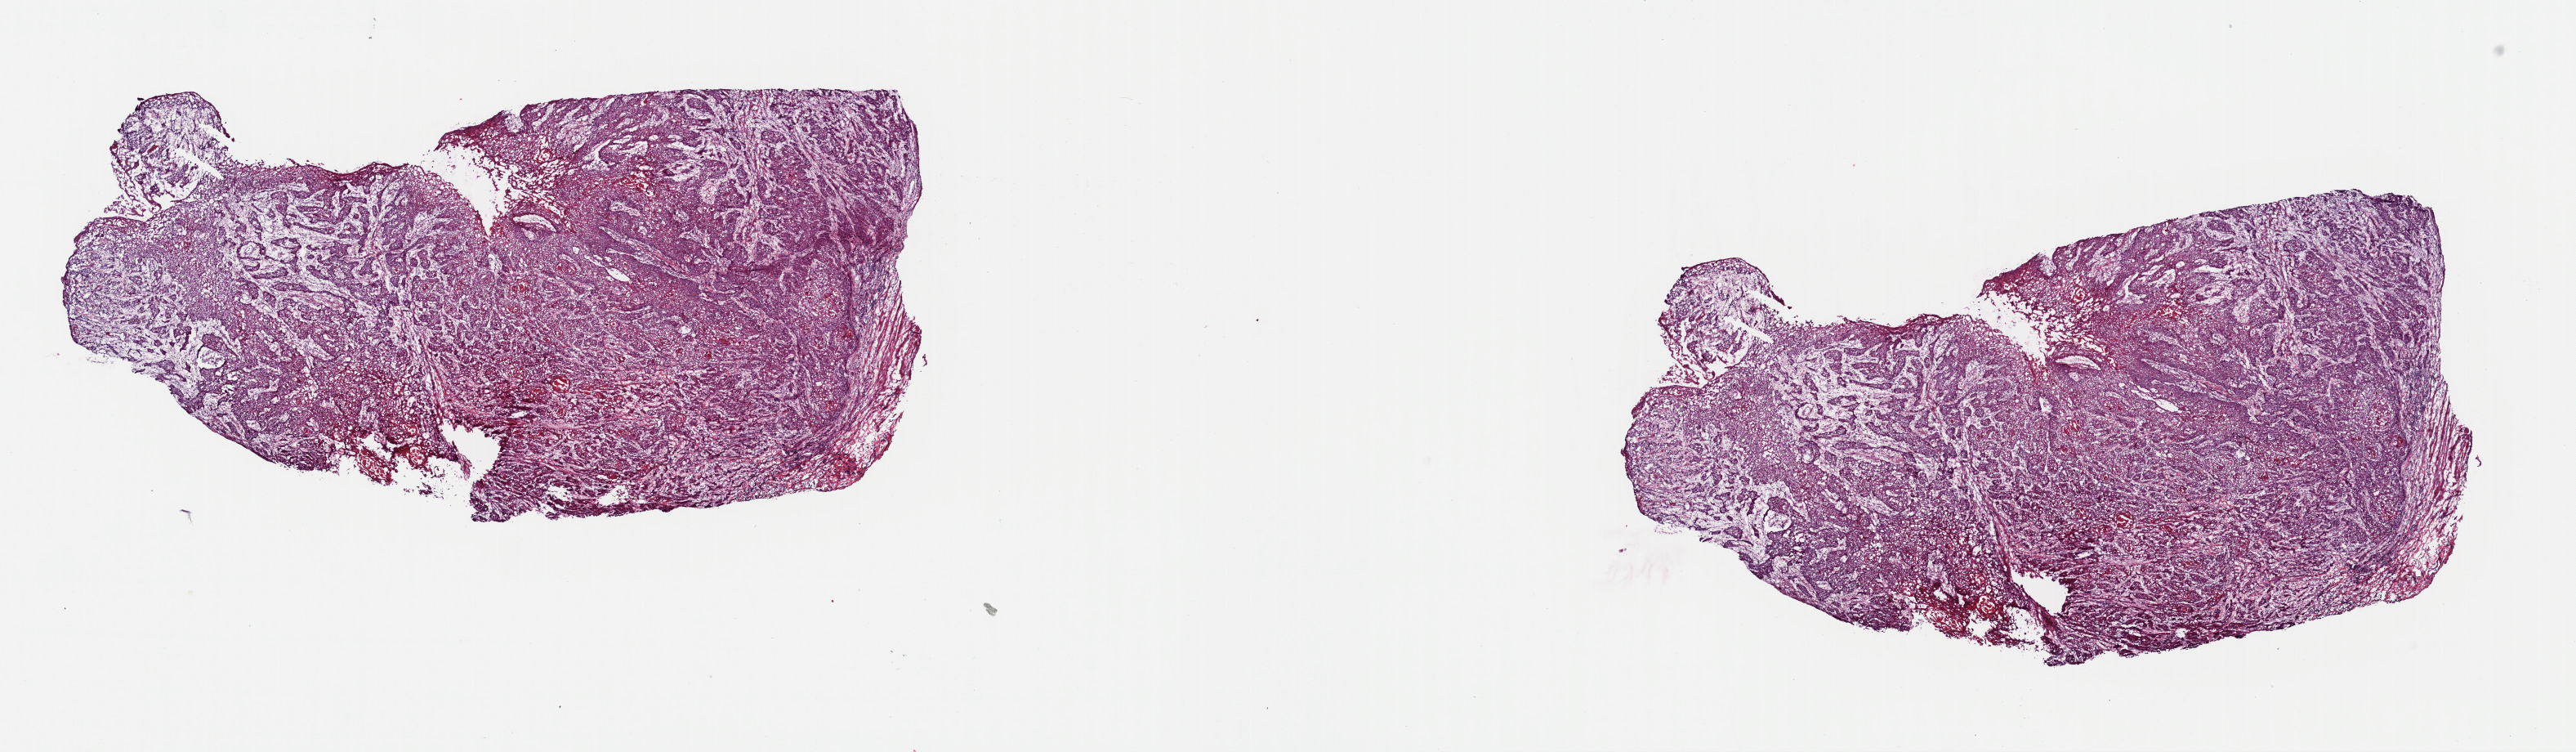
Digitized Hematoxylin and eosin (H&E) stained tissue section (whole slide) — shown as a low-resolution overview of the whole scanned area (about 24.9 x 7.3 mm). Frozen section. Esophagus, primary tumour sample. Male patient; age at initial diagnosis 58 years. Histologic grade: G1 (well differentiated). Composition of this section per pathologist review: tumour cells 97%, tumour nuclei 90%, normal cells 0%, stromal cells 0%, necrosis 3%. Infiltration values recorded for this section: lymphocyte infiltration 0%, monocyte infiltration 0%, neutrophil infiltration 0%.
Histologic diagnosis: Squamous cell carcinoma, NOS (middle third of esophagus). AJCC pathologic stage: IIA.